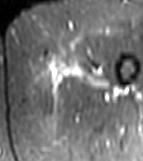
MRI of an extremity soft-tissue mass, one axial slice; position 8 of 81 along the scan axis; STIR; MR volume resampled by the dataset authors to the PET/CT grid (not the native acquisition matrix); 3.27 mm slice thickness; 143 × 161 image matrix, field of view 140 × 157 mm. Female patient. From the clinical record (not read from this slice): histological type: myxofibrosarcoma; grade: intermediate; site of the primary tumour: left thigh.
Annotated regions visible in this slice (expert contour drawn on MRI and transferred to this co-registered scan by the dataset authors):
- gross tumour volume including surrounding oedema: bounding box <42,53,109,93> (left, top, right, bottom; pixels)